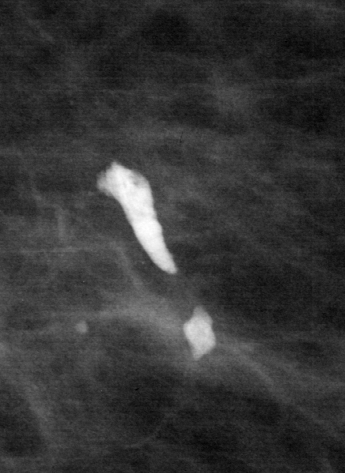
Region of interest cut from a scanned film mammogram (one marked finding); left breast; MLO view; BI-RADS breast density category 2 (scale 1–4).
Finding: calcifications, distribution linear; BI-RADS assessment category 2; pathology (as recorded): benign.